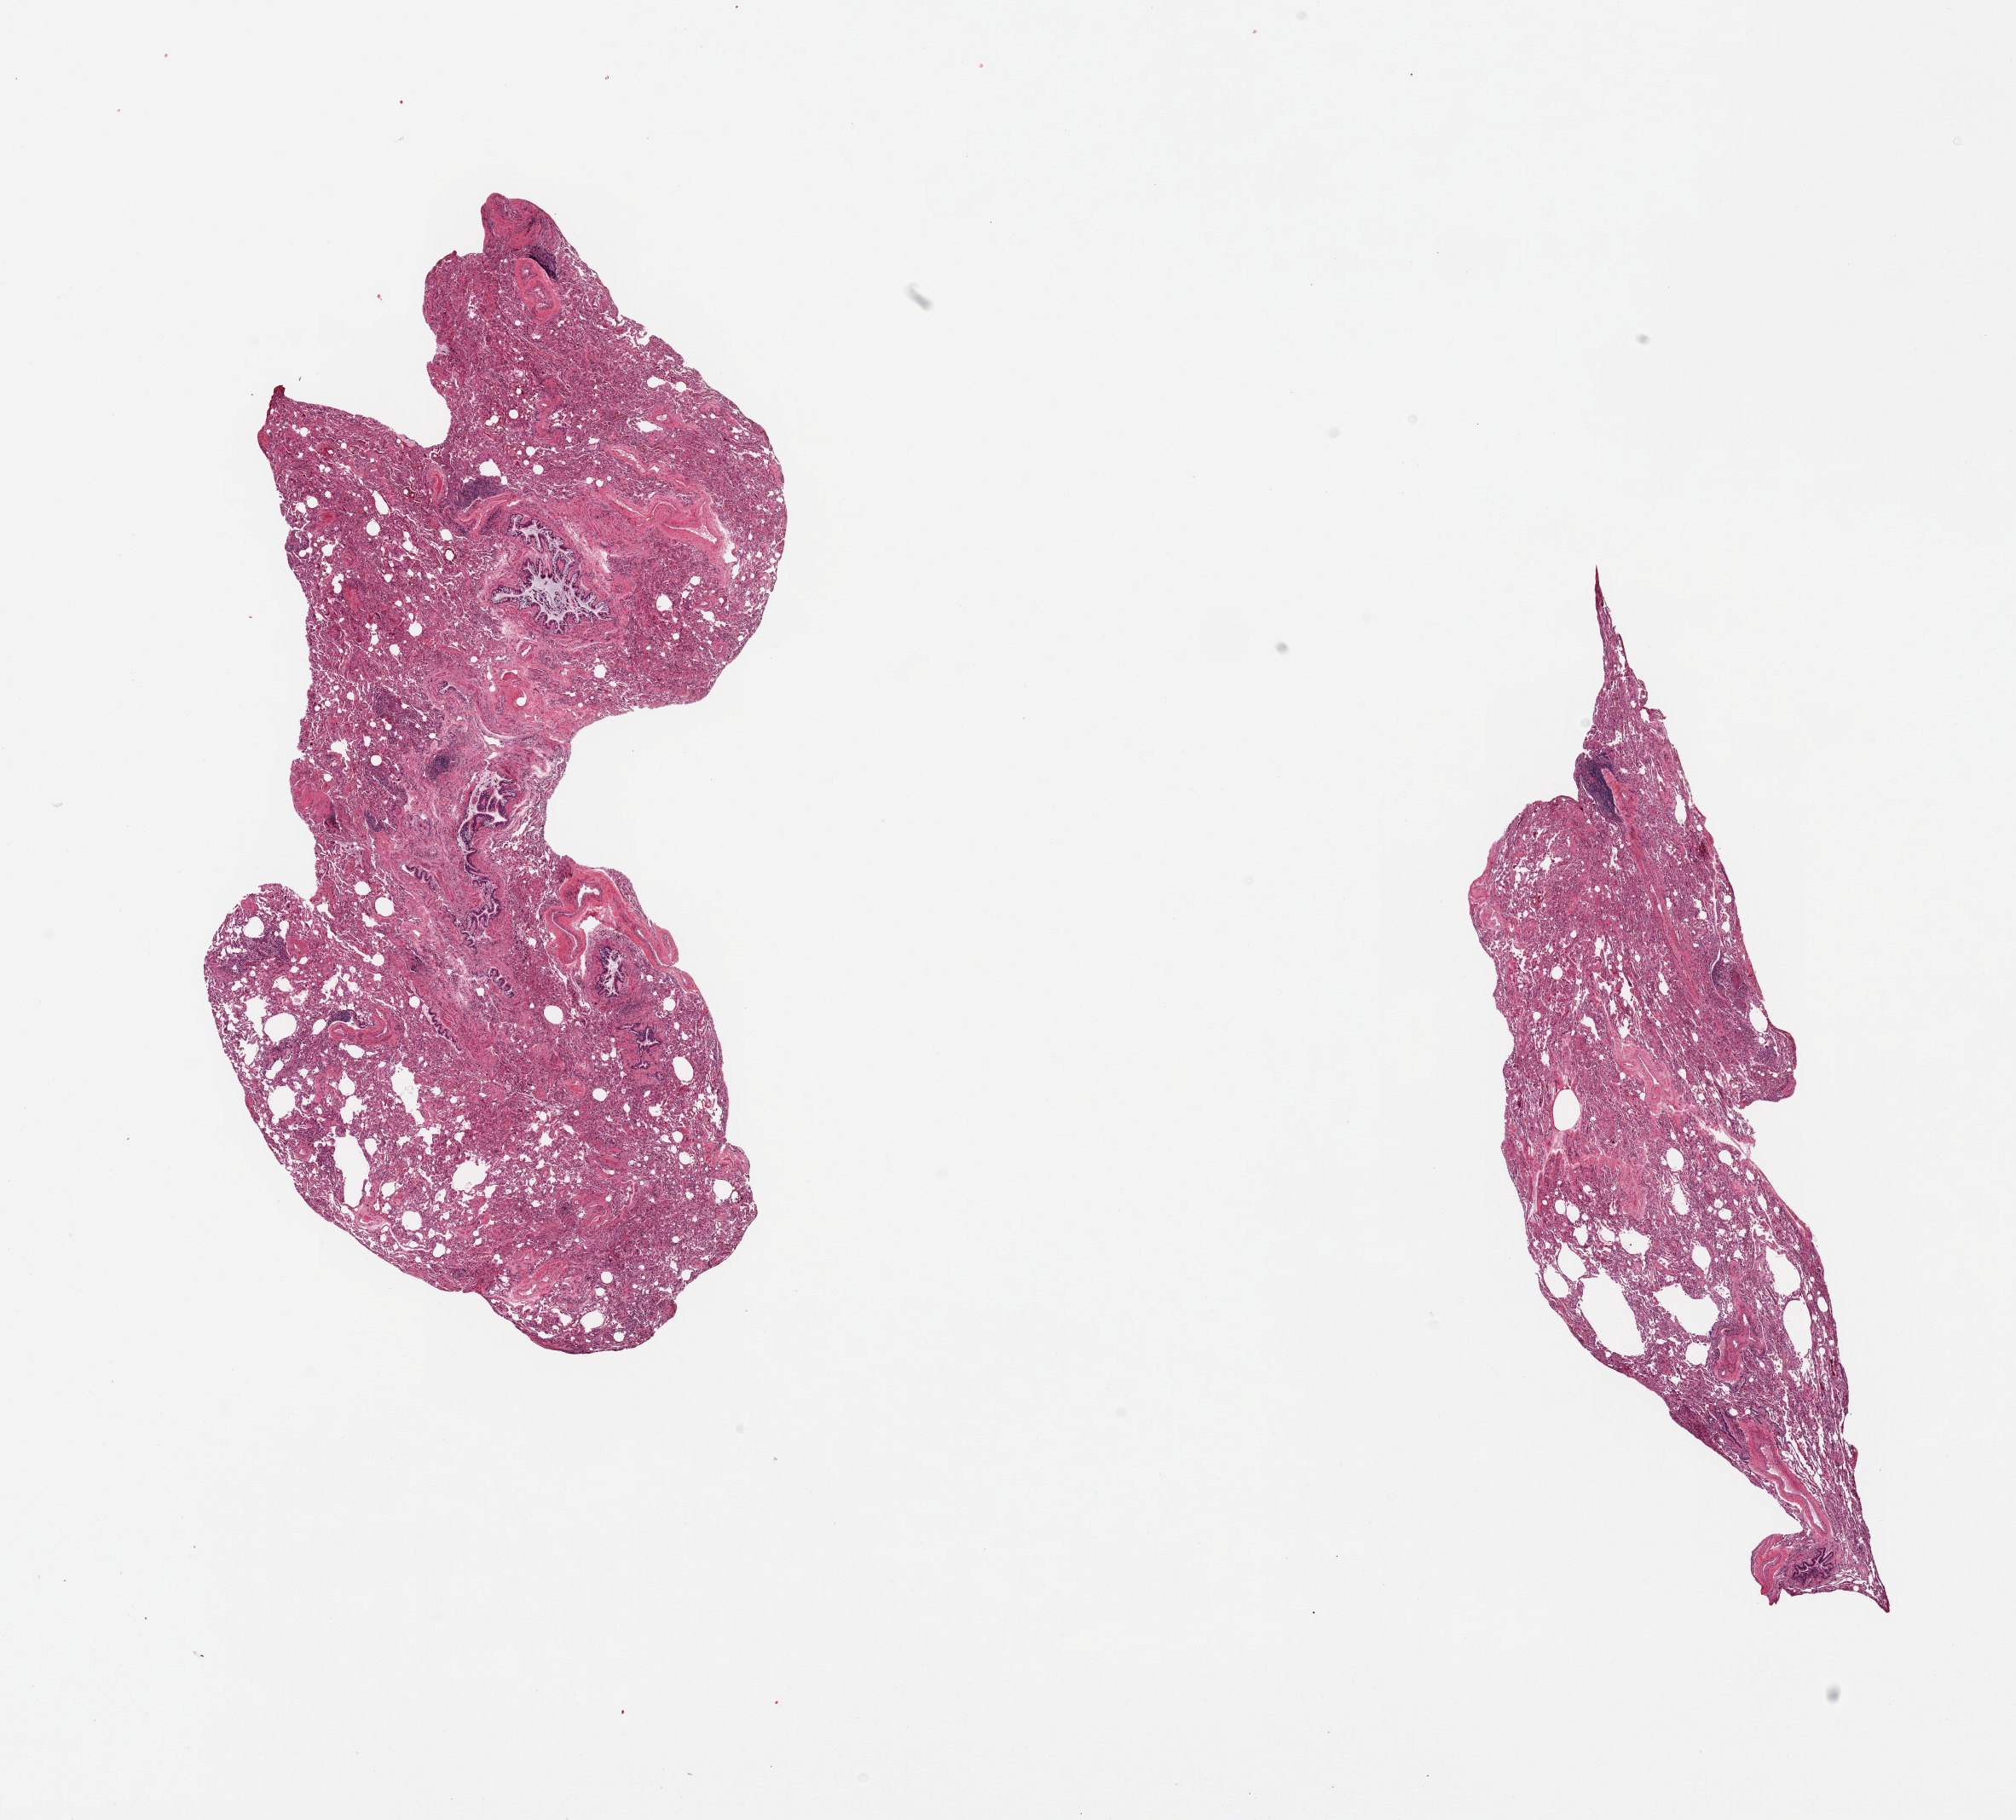
Whole-slide image, haematoxylin and eosin stain, brightfield, a low-resolution overview of the entire scanned area, about 18.7 x 16.9 mm. PAXgene-fixed paraffin-embedded (PFPE) section. Target tissue: lung. Tissue donor sample. Male donor.
• review note (as recorded): 2 pieces; atelectasis